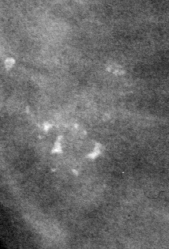
Region of interest cut from a scanned film mammogram (one marked finding); left breast; CC view; BI-RADS breast density category 2 (scale 1–4).
Calcifications, morphology pleomorphic, distribution clustered; BI-RADS assessment category 4; pathology (as recorded): benign.